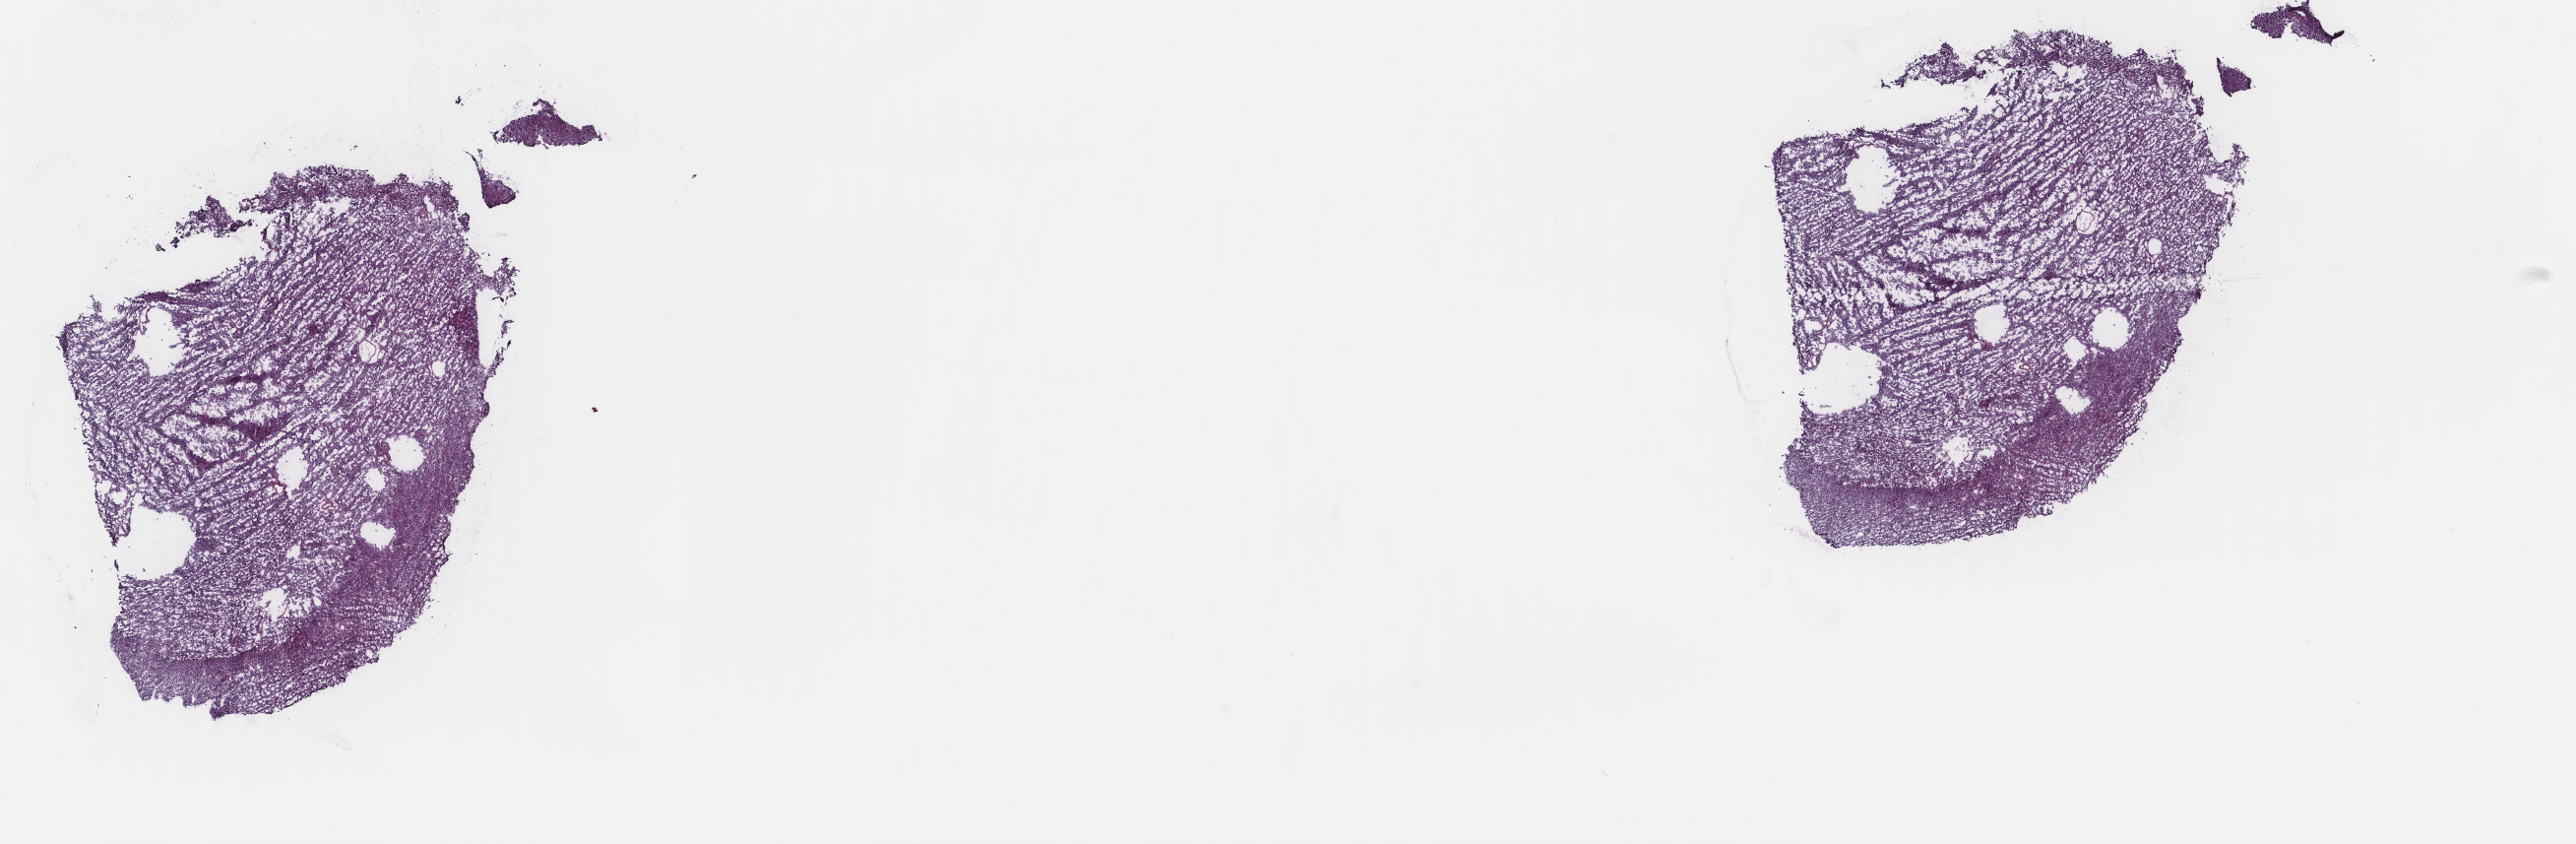
Digitized H&E tissue section (whole slide), whole scanned area (about 20.8 x 6.8 mm, from a 40x scan) shown as a low-resolution overview, frozen section, brain, primary tumour sample. Patient: male, age at initial diagnosis 34 years.
Pathologic diagnosis: Oligodendroglioma, anaplastic (frontal lobe).